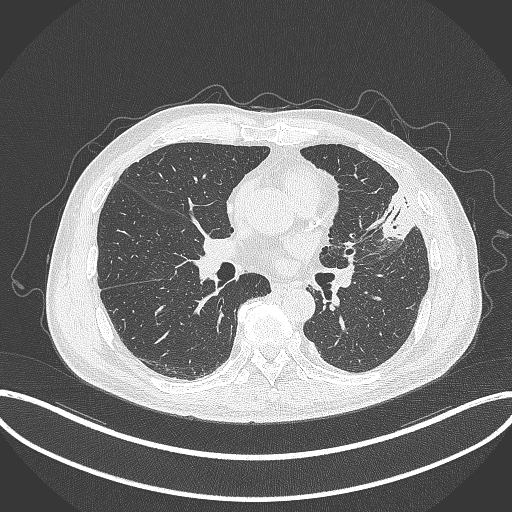
Chest CT, one axial slice. Slice 167 of 382 in the series (ordered by position). Reconstruction kernel B70f. 120 kVp. Lung window (W 1500 / L -600 HU). 512 × 512 image matrix. Patient: male, 64 years. Case-level facts recorded for this patient, not image findings: clinical TNM (as recorded): T4 N1 M0.
Outlined on this slice (rectangle marked by the reading radiologist):
- lung tumour (recorded histology: adenocarcinoma): bounding box (x1, y1, x2, y2) in pixels: (364, 178, 415, 246)